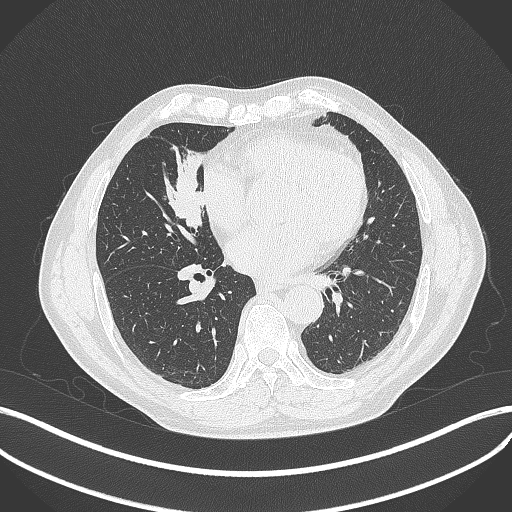
Chest CT, one axial slice; slice 172 of 429 in the series (ordered by position); reconstruction kernel B70f; lung window (W 1500 / L -600 HU); 1 mm slice thickness; 512 × 512 image matrix. Patient: male, 61 years. From the clinical record (not read from this slice): clinical TNM (as recorded): T2b N1 M0.
Annotated regions visible in this slice (rectangle marked by the reading radiologist):
- lung tumour (recorded histology: squamous cell carcinoma): bounding box <155,141,210,230> (left, top, right, bottom; pixels)